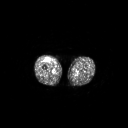
FDG PET of an extremity soft-tissue mass (from a PET/CT study), one axial slice. Slice 241 of 311 in the series (ordered by position). 3.27 mm slice thickness. 128 × 128 image matrix. Patient: male, 56 years. Case-level facts recorded for this patient, not image findings: histological type: pleiomorphic leiomyosarcoma; grade: intermediate; site of the primary tumour: right thigh.
Outlined on this slice (expert contour drawn on MRI and transferred to this co-registered scan by the dataset authors):
- gross tumour volume including surrounding oedema: bounding box <45,57,51,62> (left, top, right, bottom; pixels)